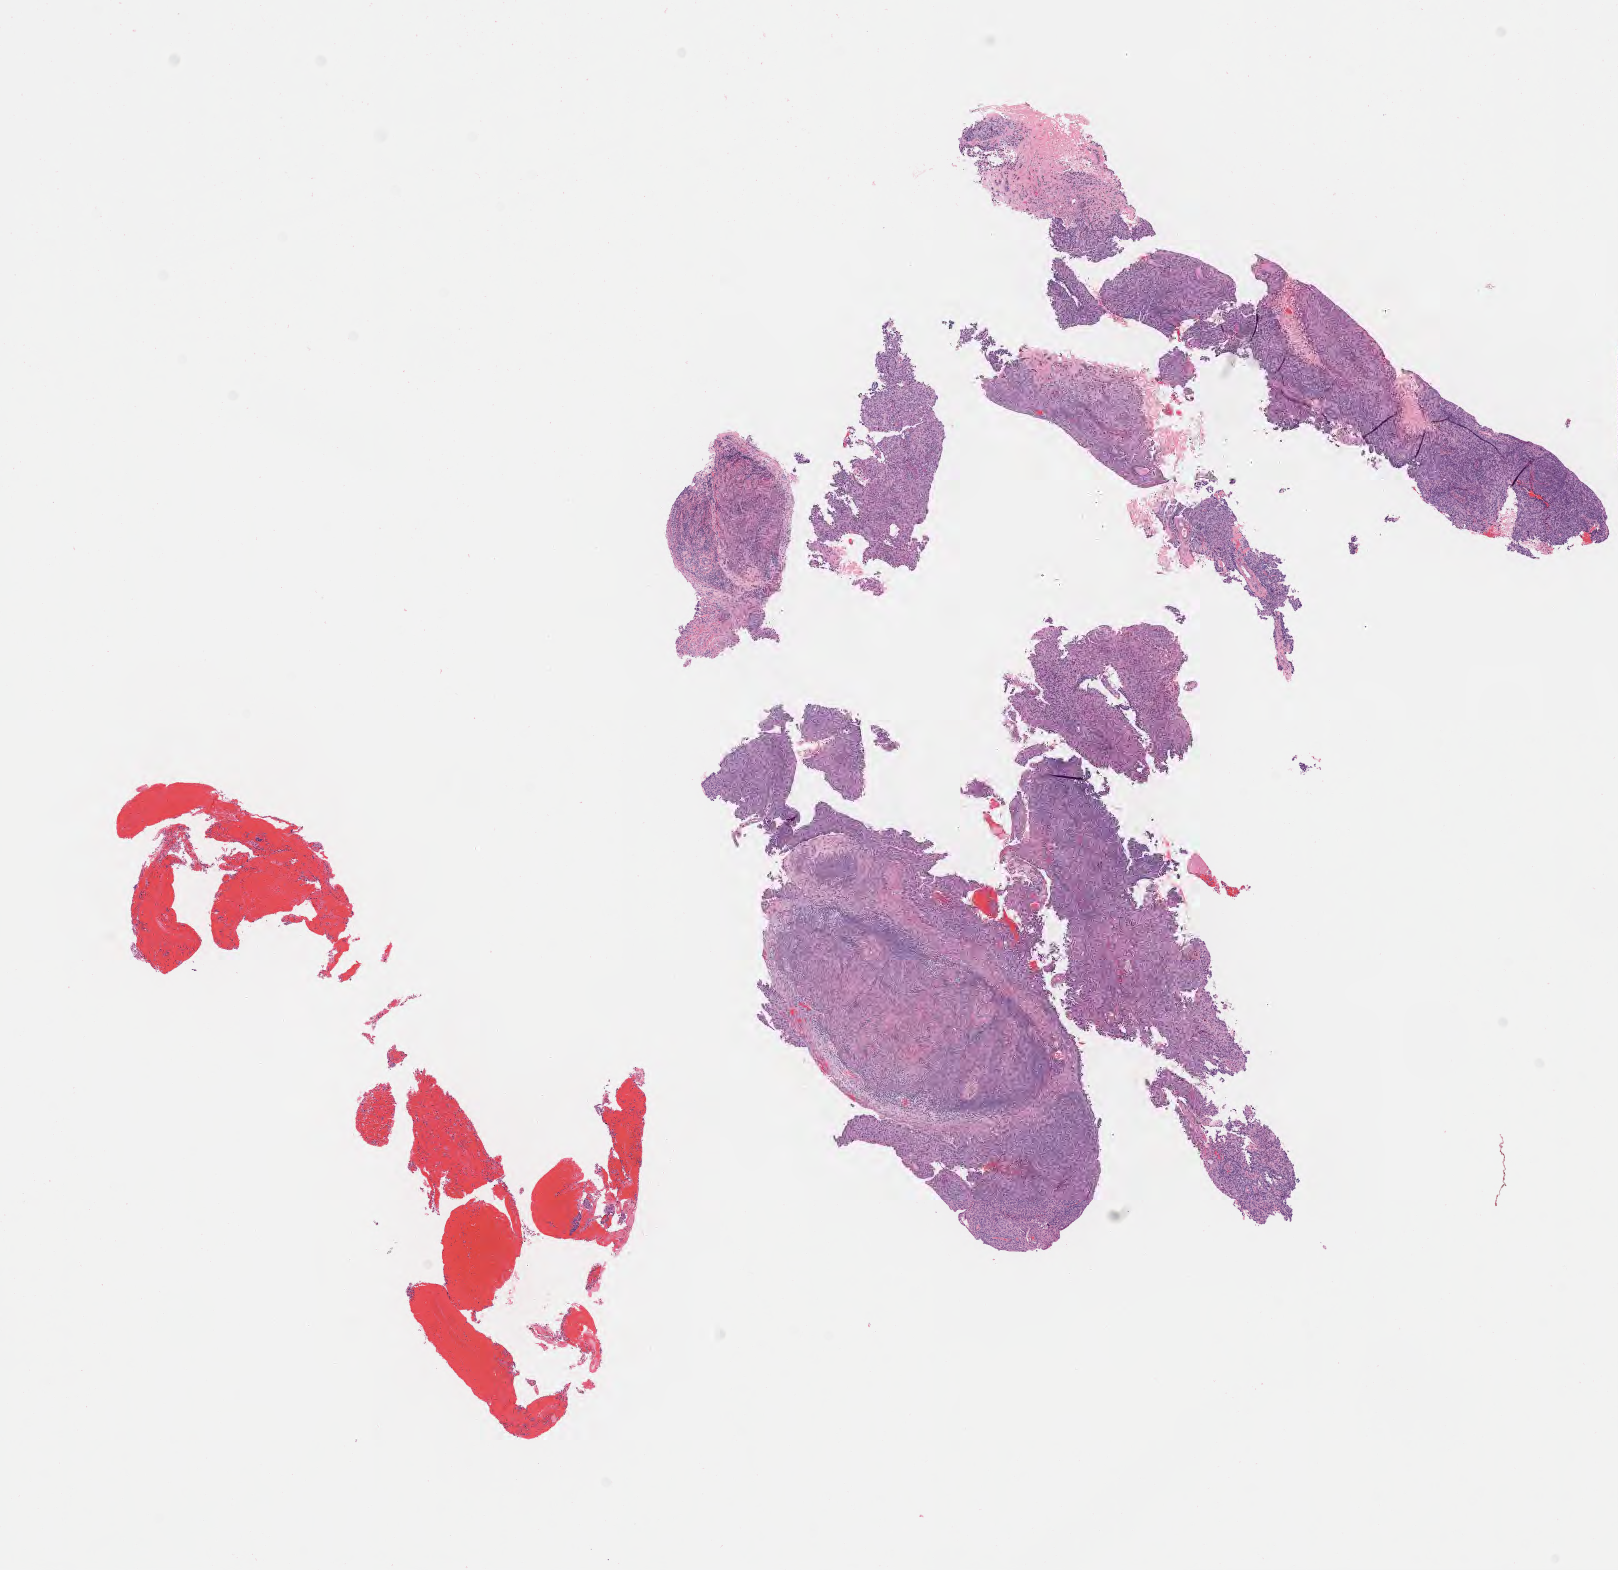
Whole-slide image, hematoxylin and eosin (H&E) stain, low-resolution overview of the scanned area, about 13.1 x 12.7 mm; tumor tissue; site: cervix. Patient: female, 68 years old.
- diagnosis: Squamous cell carcinoma, large cell, nonkeratinizing, NOS